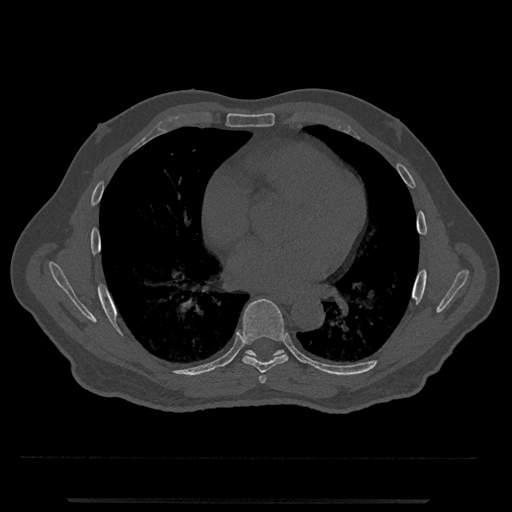
CT including the spine, one axial slice; slice 671 of 797 in the series (ordered by position); reconstruction kernel Br40s/3; bone window (W 1800 / L 400 HU); 0.5 mm slice thickness; 512 × 512 image matrix, field of view 419 × 419 mm. Patient: male, 63 years. Case-level facts recorded for this patient, not image findings: primary cancer: prostate.
Structures marked on this image (semi-automatically segmented with operator editing):
- T6 vertebra: bounding box <259,375,267,383> (left, top, right, bottom; pixels)
- T7 vertebra: <237,298,289,373>
- T8 vertebra: <245,350,285,357>